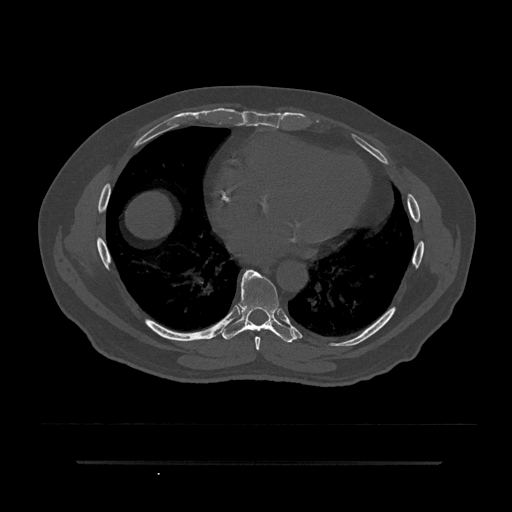
CT including the spine, one axial slice; position 442 of 797 along the scan axis; 120 kVp; bone window (W 1800 / L 400 HU); 512 × 512 image matrix. Patient: male, 59 years. Case-level facts recorded for this patient, not image findings: primary cancer: bile ducts.
Annotated regions visible in this slice (semi-automatic segmentation, software-assisted and operator-edited):
- T7 vertebra: bounding box [x1, y1, x2, y2] px = [243, 271, 261, 350]
- T8 vertebra: [222, 270, 295, 343]